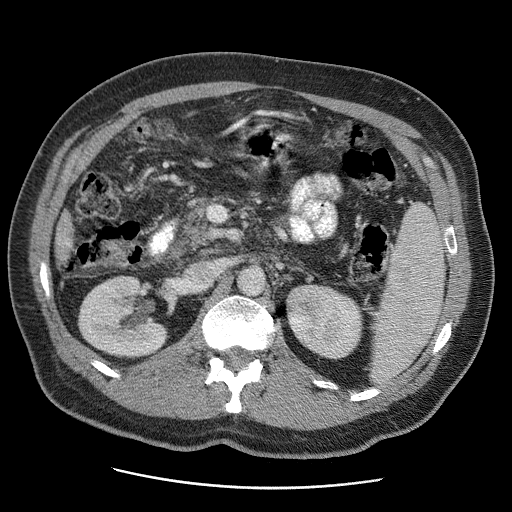
Contrast-enhanced abdominal CT (liver protocol), one axial slice. Slice 8 of 81 in the series (ordered by position). Reconstruction kernel STANDARD. 120 kVp. Soft-tissue window (W 400 / L 40 HU). 512 × 512 image matrix, field of view 380 × 380 mm. From the clinical record (not read from this slice): diagnosis: hepatocellular carcinoma (patient treated with transarterial chemoembolisation; whether this scan precedes or follows treatment is not stated here); TNM stage (as recorded): Stage-IIIA; Child-Pugh class: A; tumour size: 5.5 cm.
Structures marked on this image (semi-automatically segmented with operator editing):
- liver parenchyma outside the tumour (the mass and vessels are separate outlines, so this box may not span the whole liver): box from (x=56, y=212) to (x=73, y=264) px